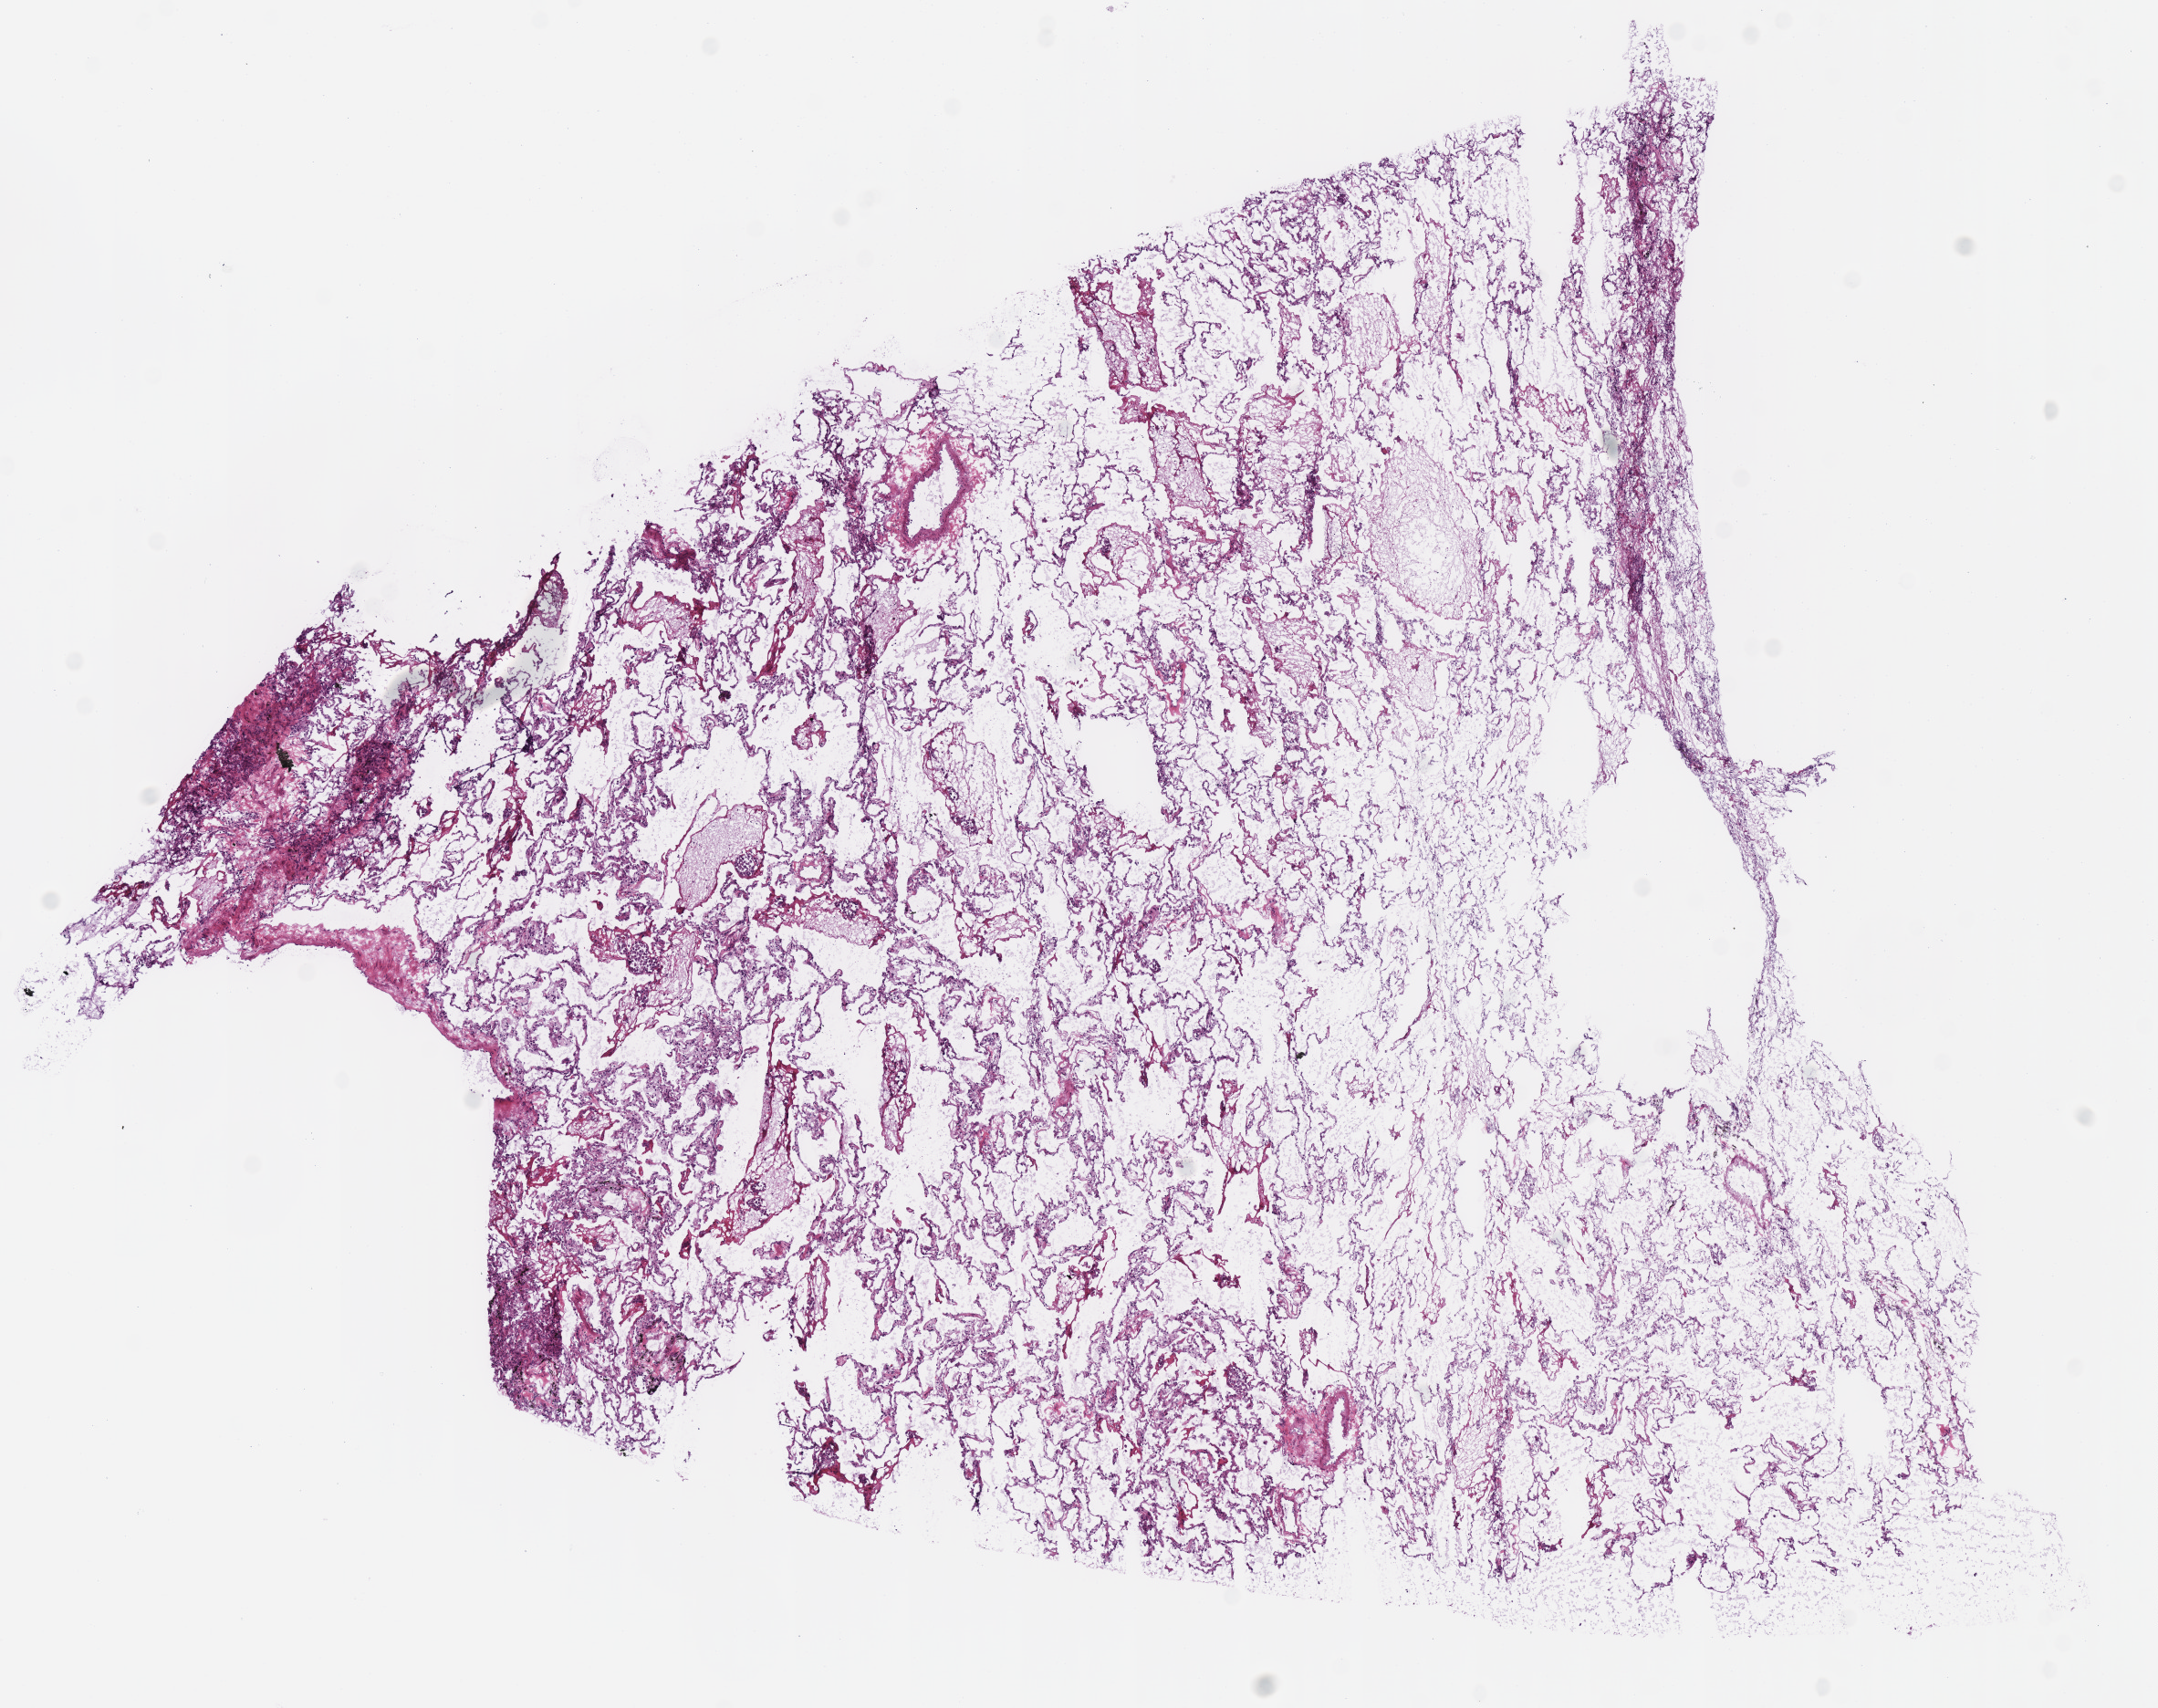
Digitized H&E tissue section (whole slide) — shown as a low-resolution overview of the whole scanned area (about 9.3 x 7.4 mm); frozen section from the top of the tissue portion; lung, solid tissue normal (non-tumour tissue) sample. Patient: male, age at initial diagnosis 79 years.
* this section: solid tissue normal (non-tumour) sample from the same patient
* patient diagnosis: Squamous cell carcinoma, NOS (upper lobe, lung)